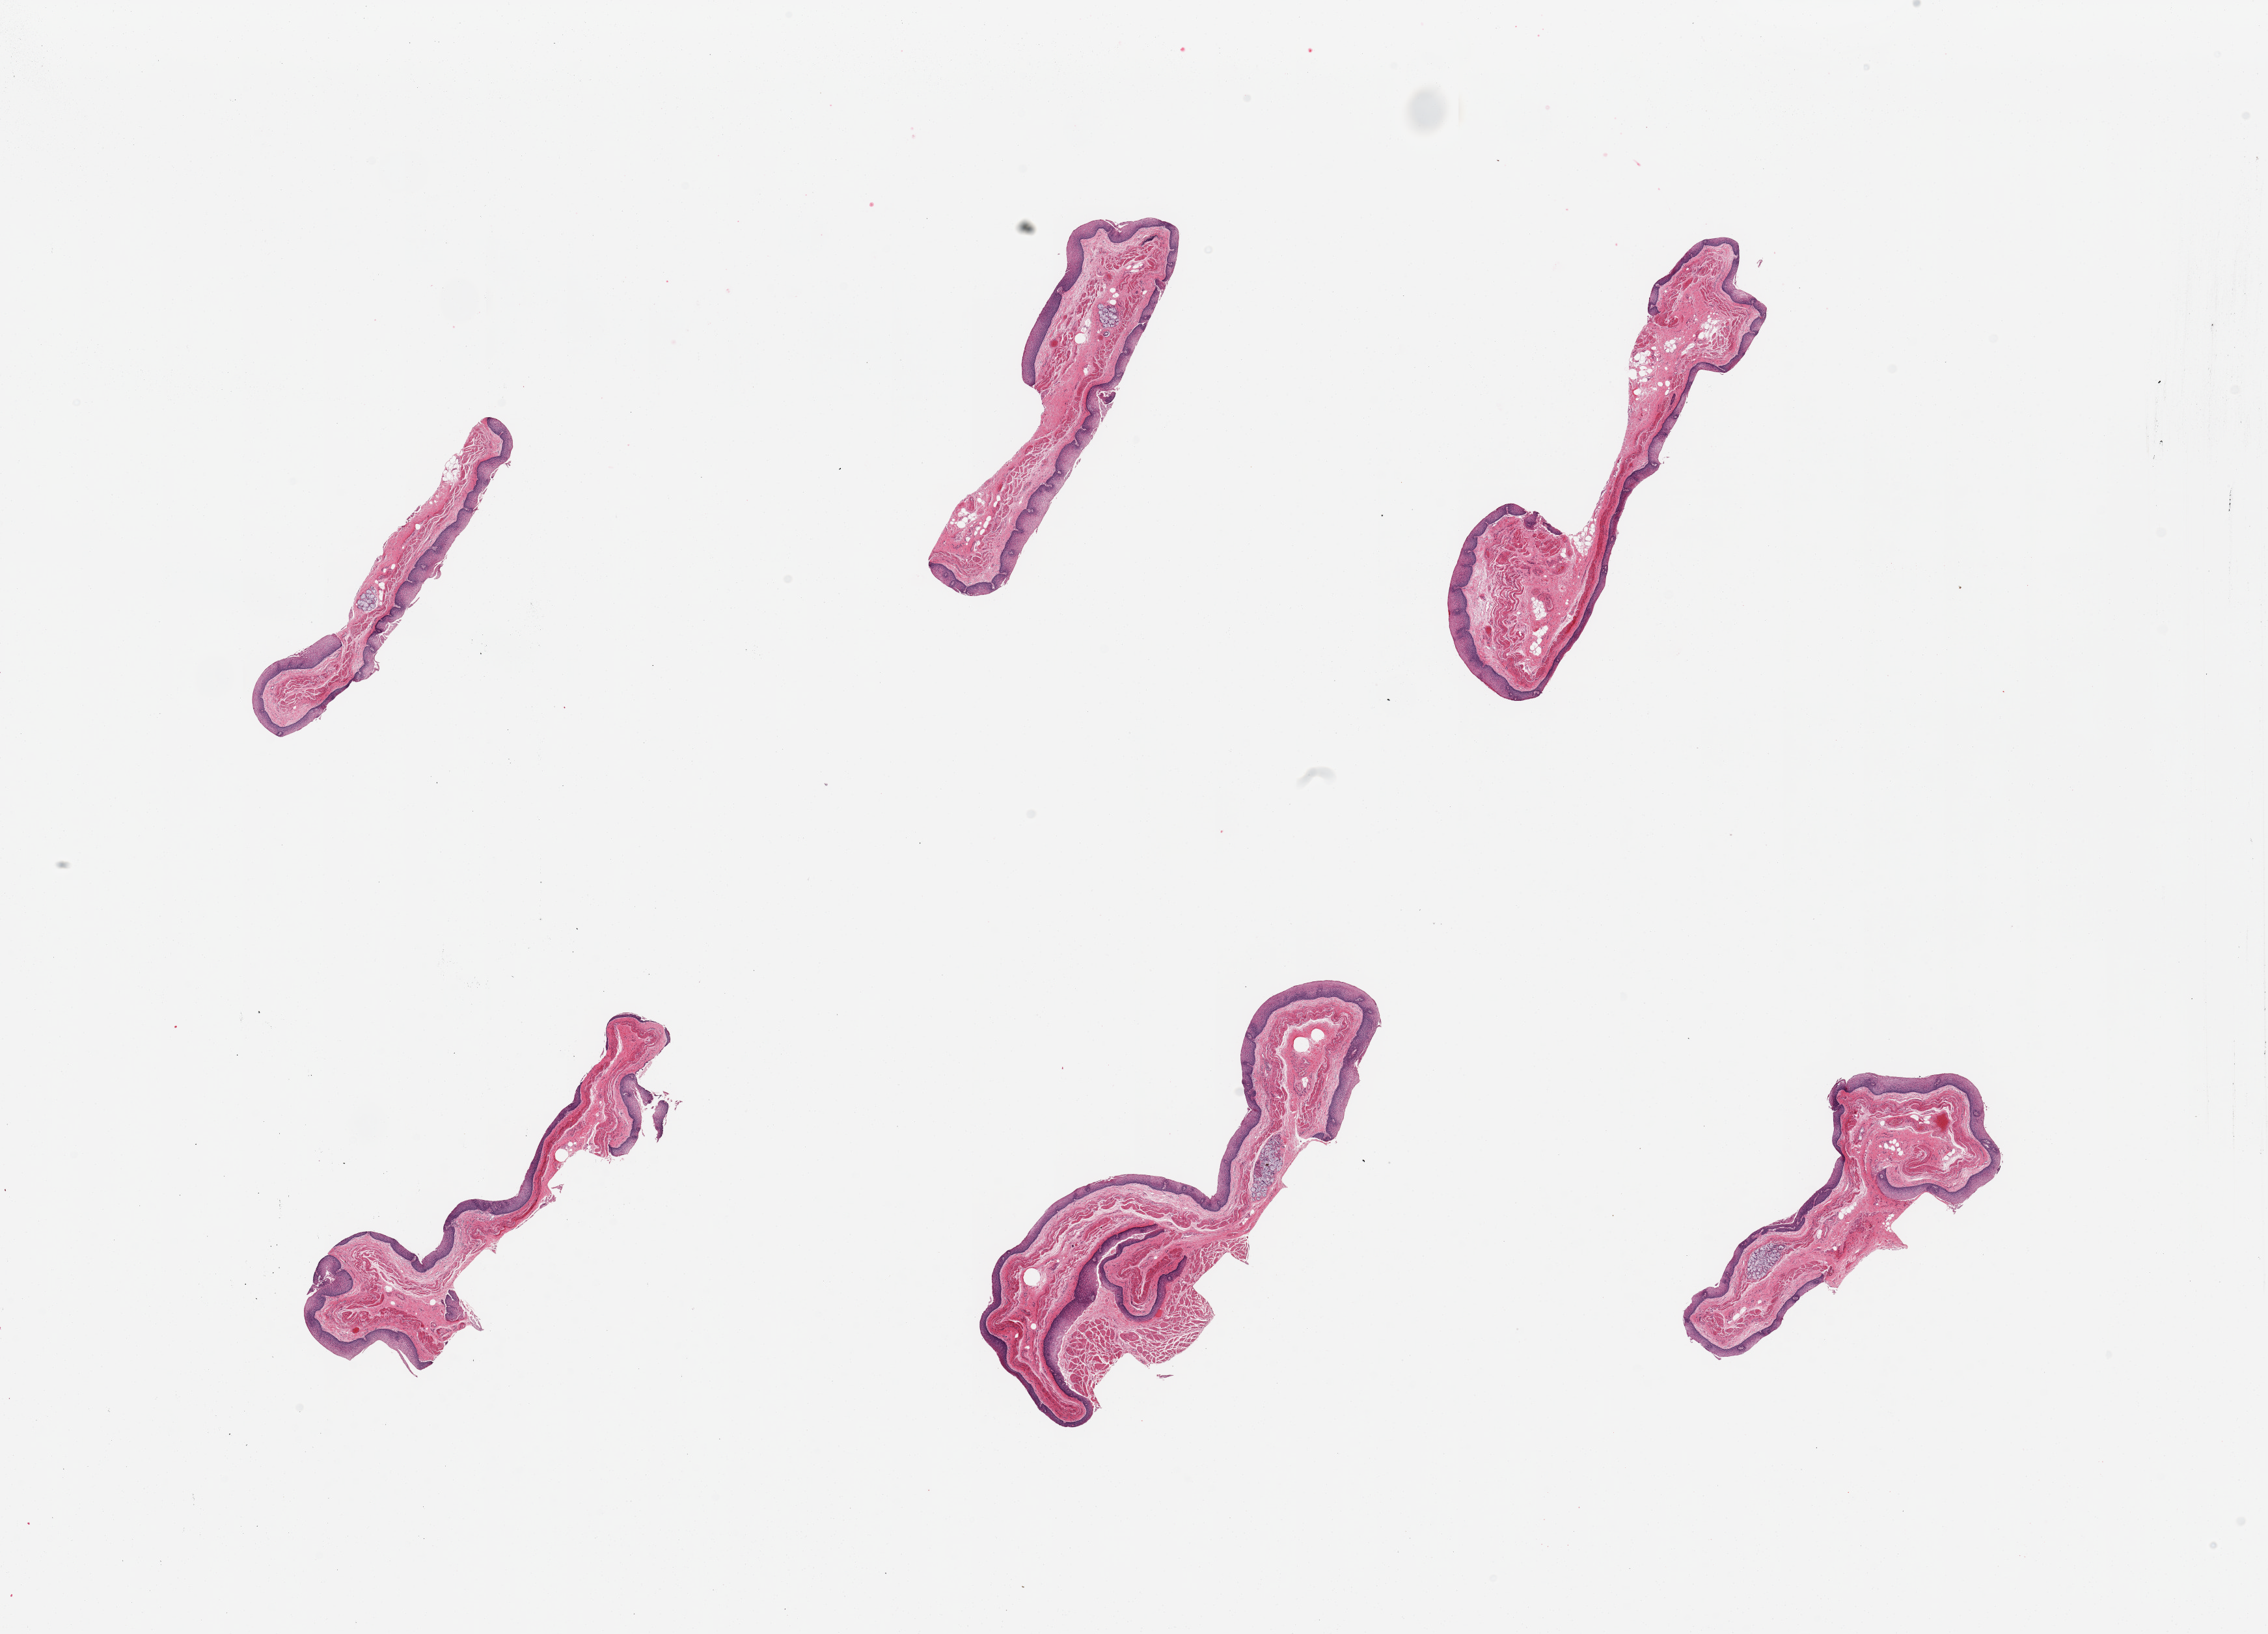
Whole-slide image, hematoxylin and eosin (H&E) stain, shown as a low-resolution overview of the whole scanned area (about 27.6 x 19.9 mm). PAXgene-fixed, paraffin-embedded tissue. Section of esophageal mucous membrane (target tissue). Donor tissue sample. Male donor.
Pathologist's review note for this sample: 6 pieces; well dissected.